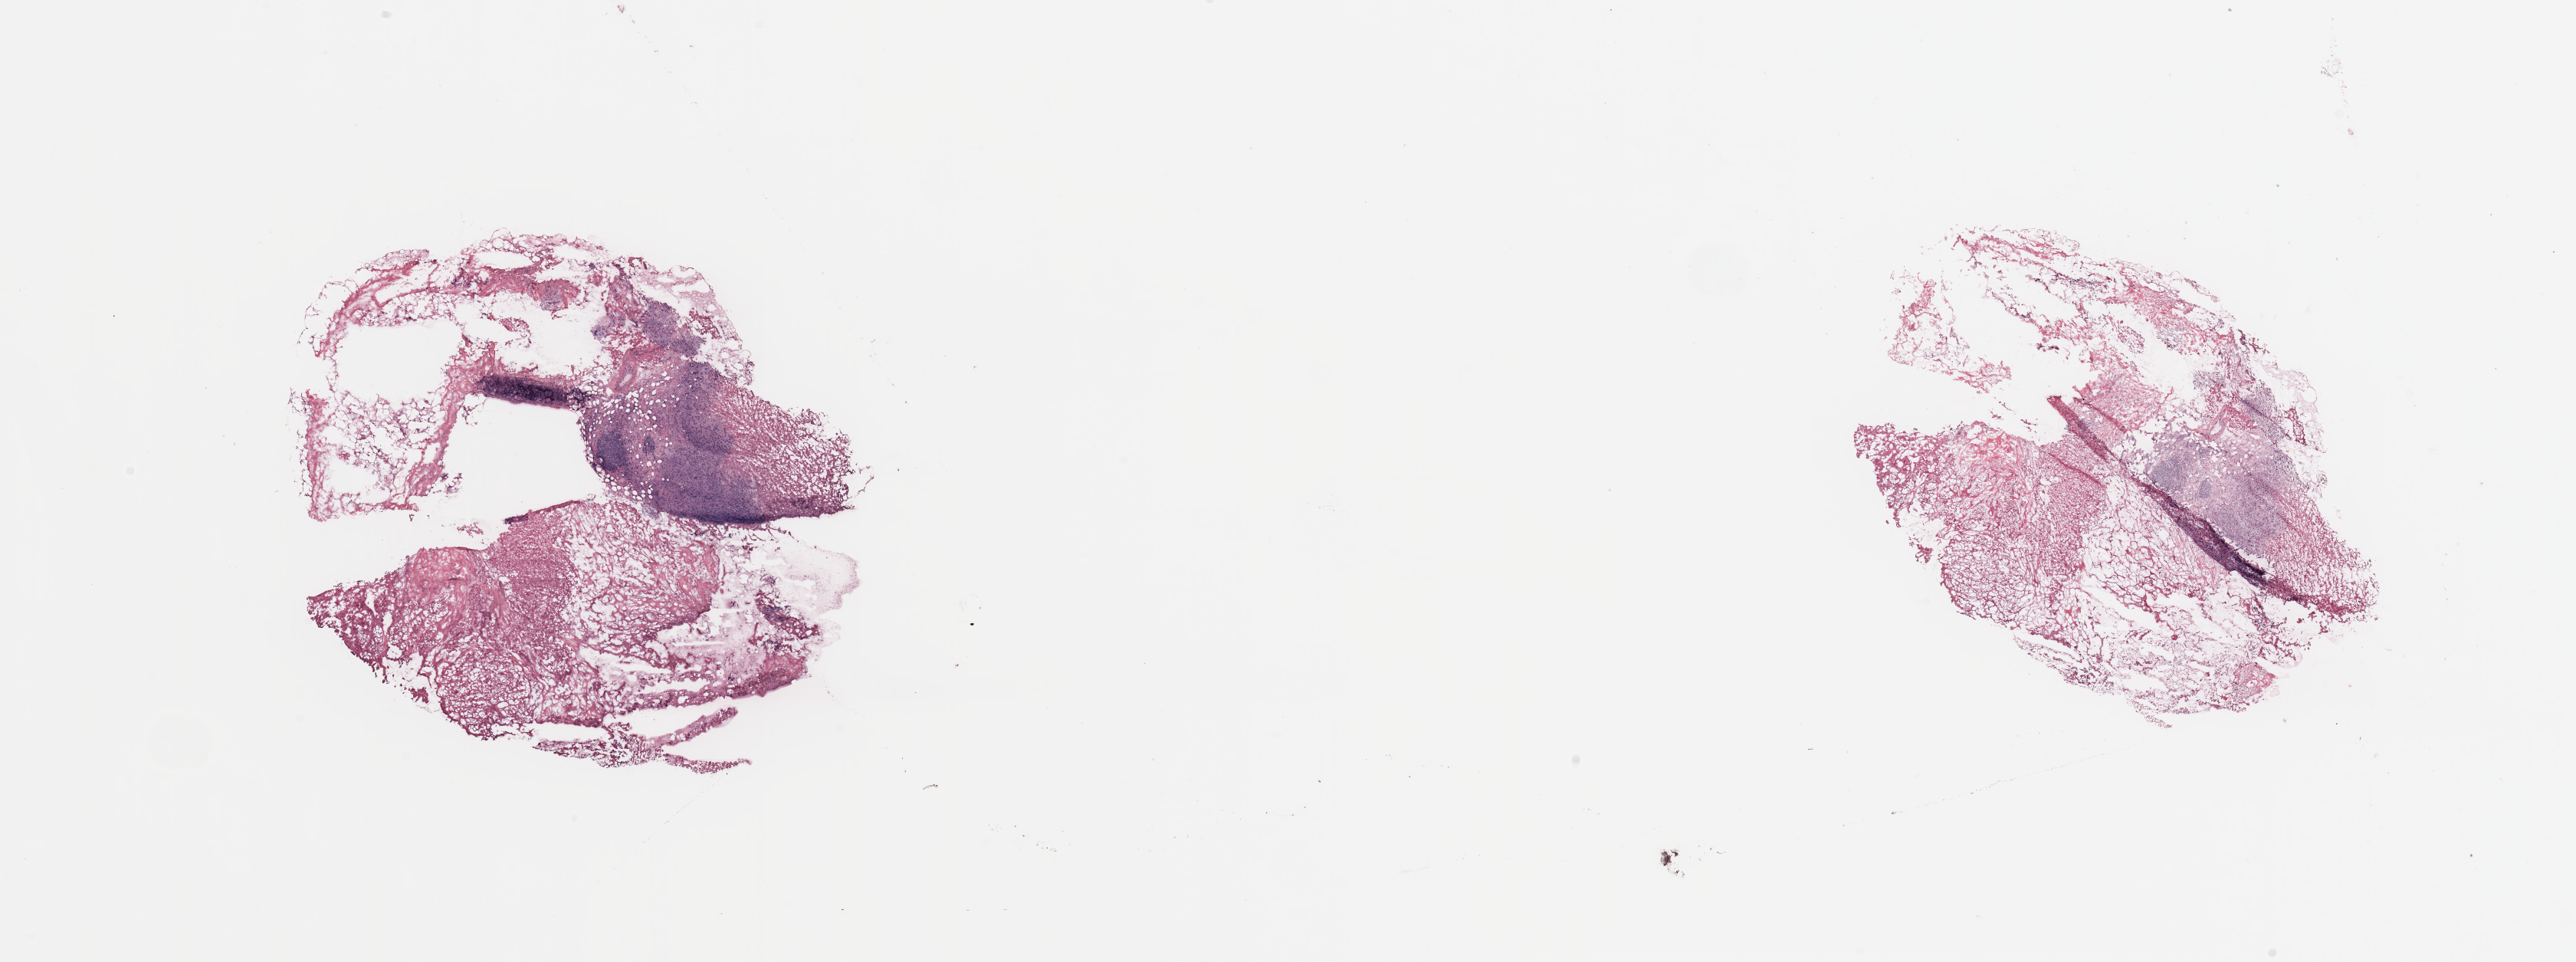
Digitized H&E-stained tissue section (whole slide) — a low-resolution overview of the entire scanned area, about 26.6 x 9.9 mm; breast, tissue type not recorded.
Patient diagnosis (cohort enrolment): breast cancer (breast).